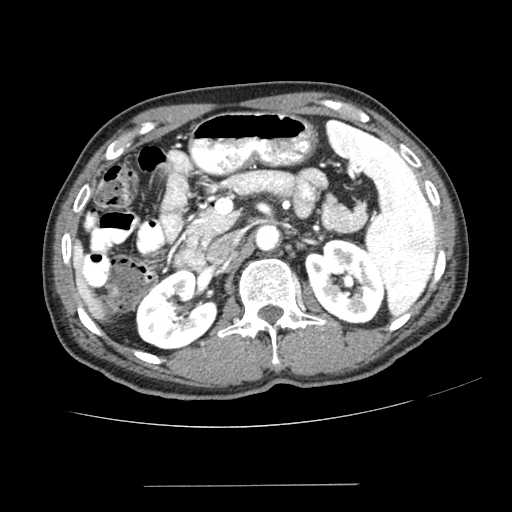
Contrast-enhanced abdominal CT (liver protocol), one axial slice. Position 135 of 187 along the scan axis. One of 2 acquisitions stored at this slice position. Soft-tissue window (W 400 / L 40 HU). 2.5 mm slice thickness. 512 × 512 image matrix, field of view 360 × 360 mm. From the clinical record (not read from this slice): diagnosis: hepatocellular carcinoma (patient treated with transarterial chemoembolisation; whether this scan precedes or follows treatment is not stated here); TNM stage (as recorded): Stage-I; Child-Pugh class: A; tumour differentiation: poorly differentiated; tumour nodularity: uninodular.
Outlined on this slice (semi-automatically segmented with operator editing):
- liver parenchyma outside the tumour (the mass and vessels are separate outlines, so this box may not span the whole liver): bounding box [x1, y1, x2, y2] px = [72, 240, 104, 318]
- liver vessels: [76, 250, 81, 259]